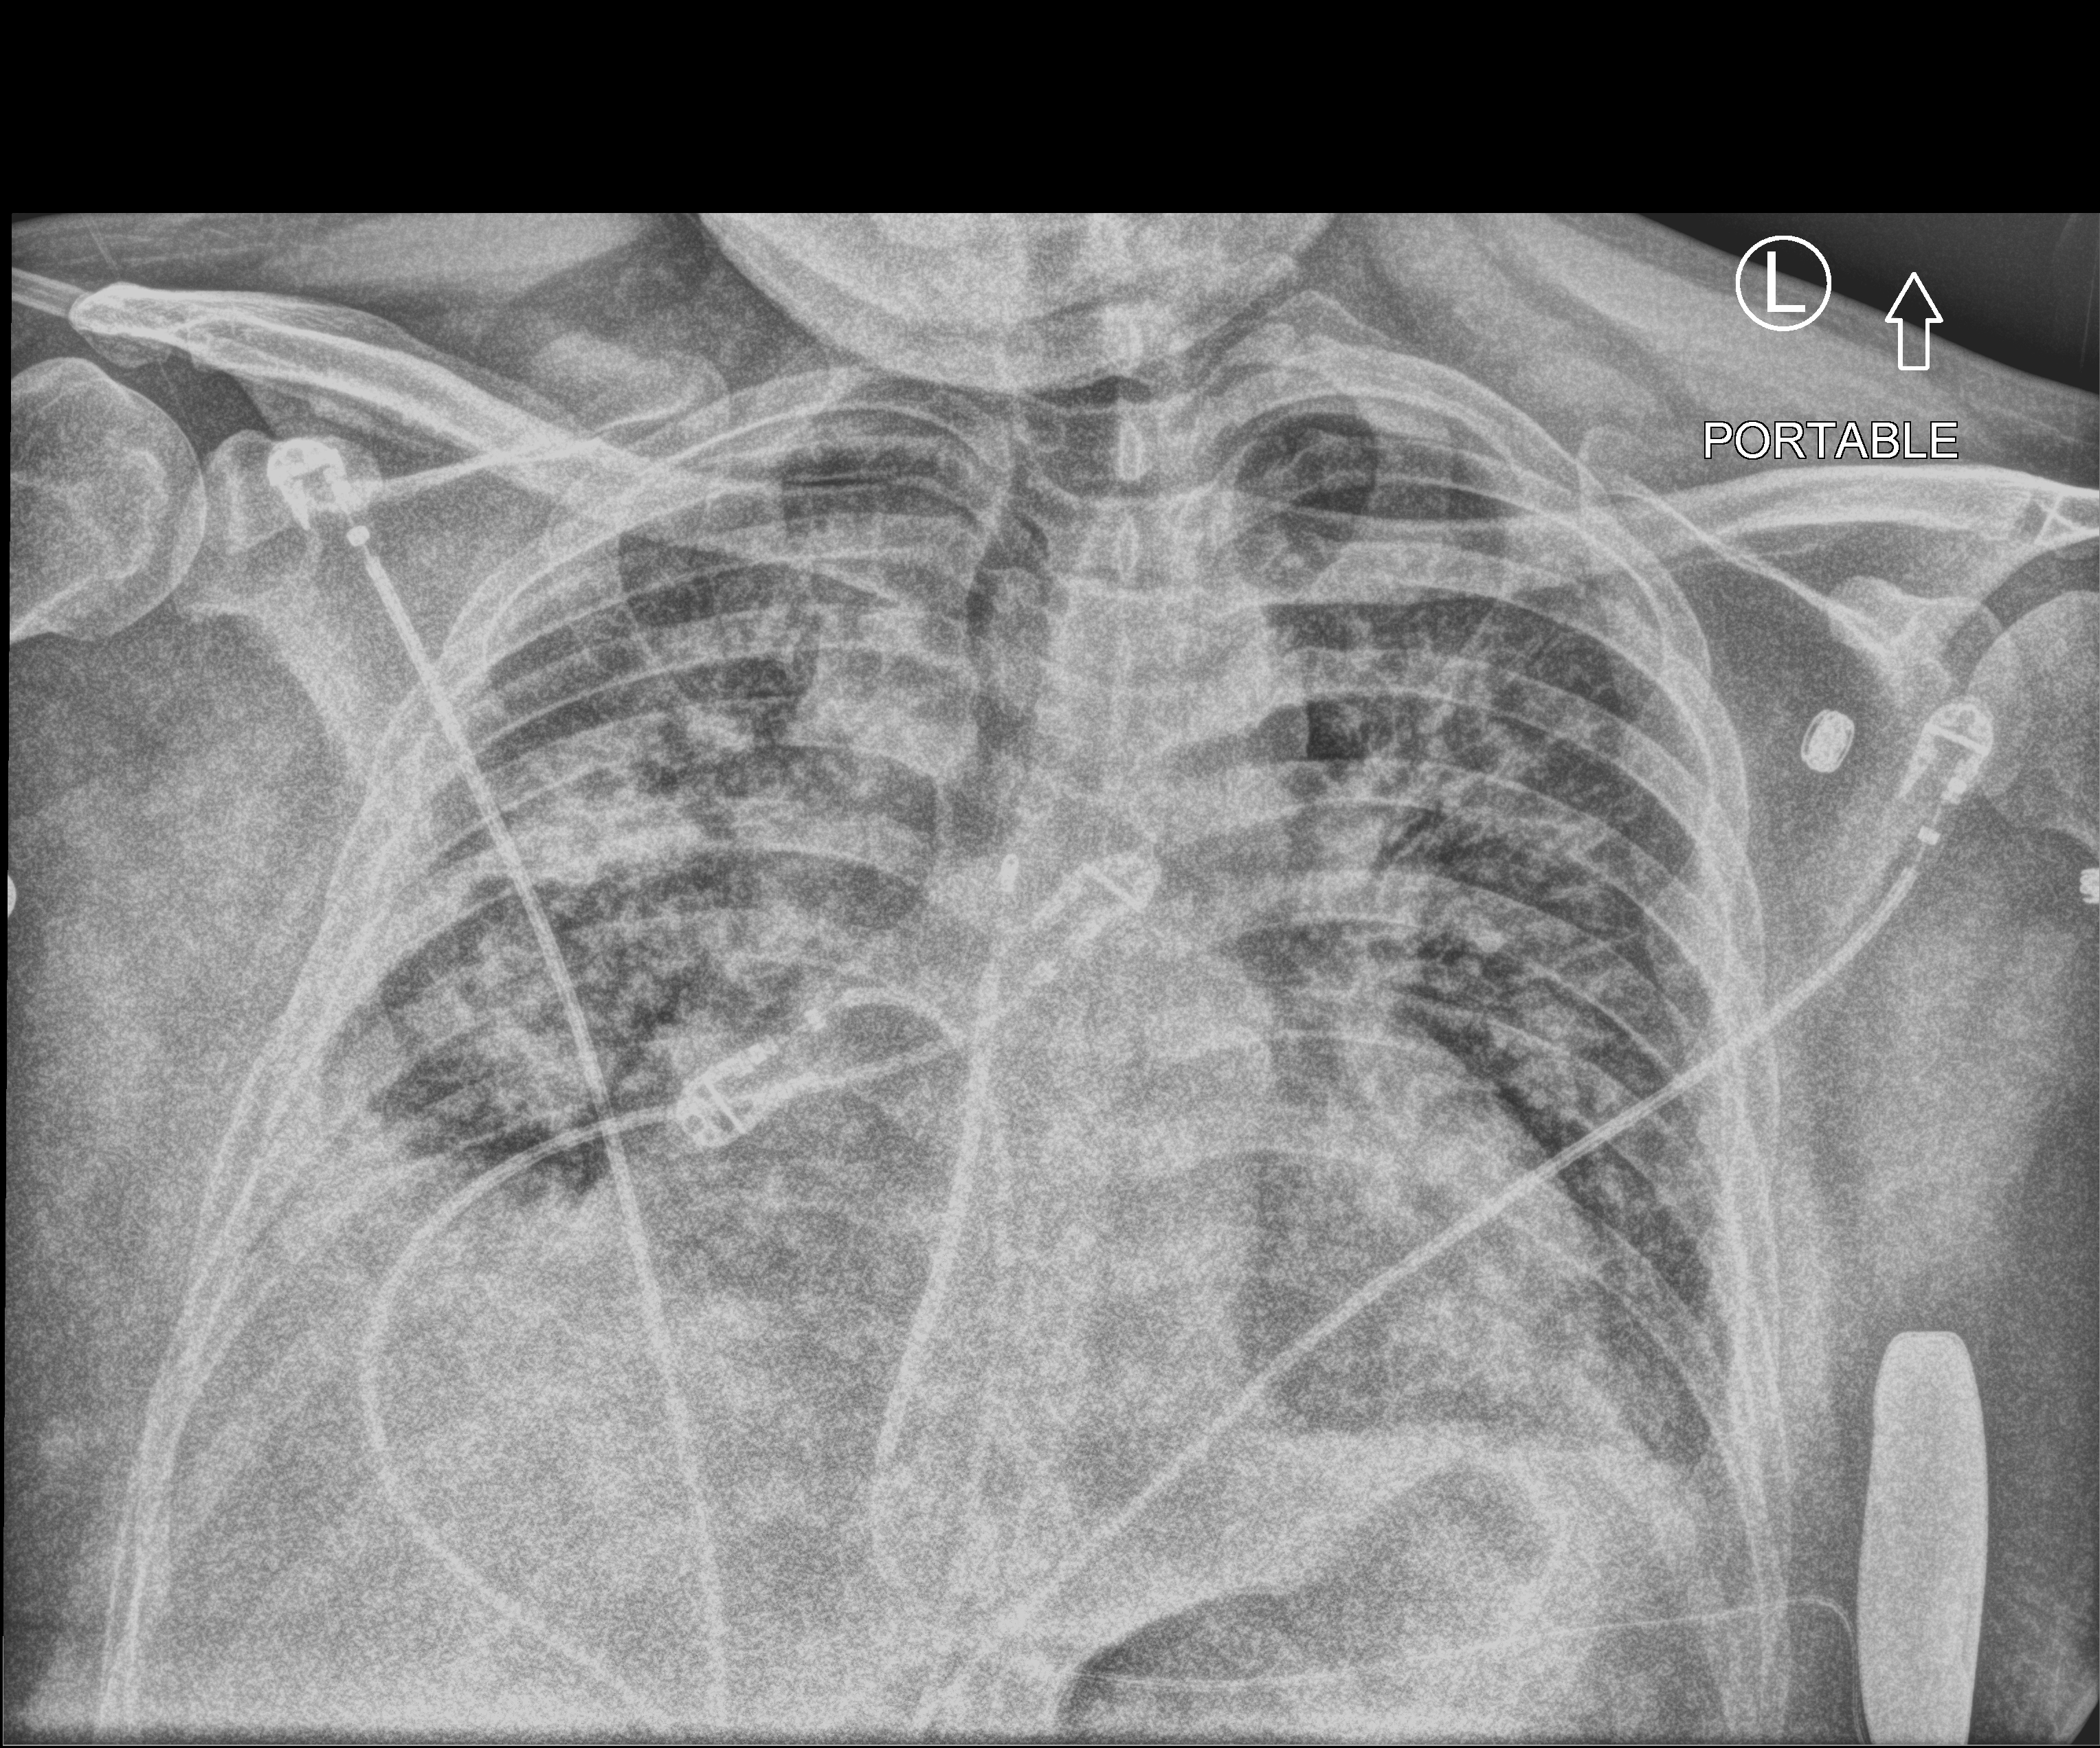
Bedside chest radiograph (computed radiography); anteroposterior (AP) projection. Patient hospitalised with COVID-19; male, aged 18–59 years.
Admission-level facts for this patient (not findings on this image; timing relative to this image not recorded):
- admitted to intensive care during this hospital stay: no
- mechanically ventilated during this hospital stay: no
- chronic kidney disease (admission record): no